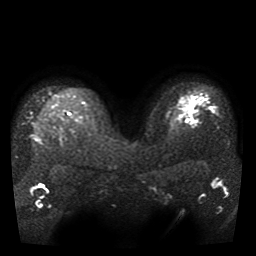
Breast MRI, one axial slice; slice 30 of 41 in the series (ordered by position); diffusion-weighted series; image 2 of 4 stored at this slice position (different b-values; order by instance number); 1.5 T; 256 × 256 image matrix, field of view 330 × 330 mm. Female patient.
Structures marked on this image (manually delineated by an expert):
- tumour on diffusion-weighted imaging: box from (x=186, y=119) to (x=197, y=123) px